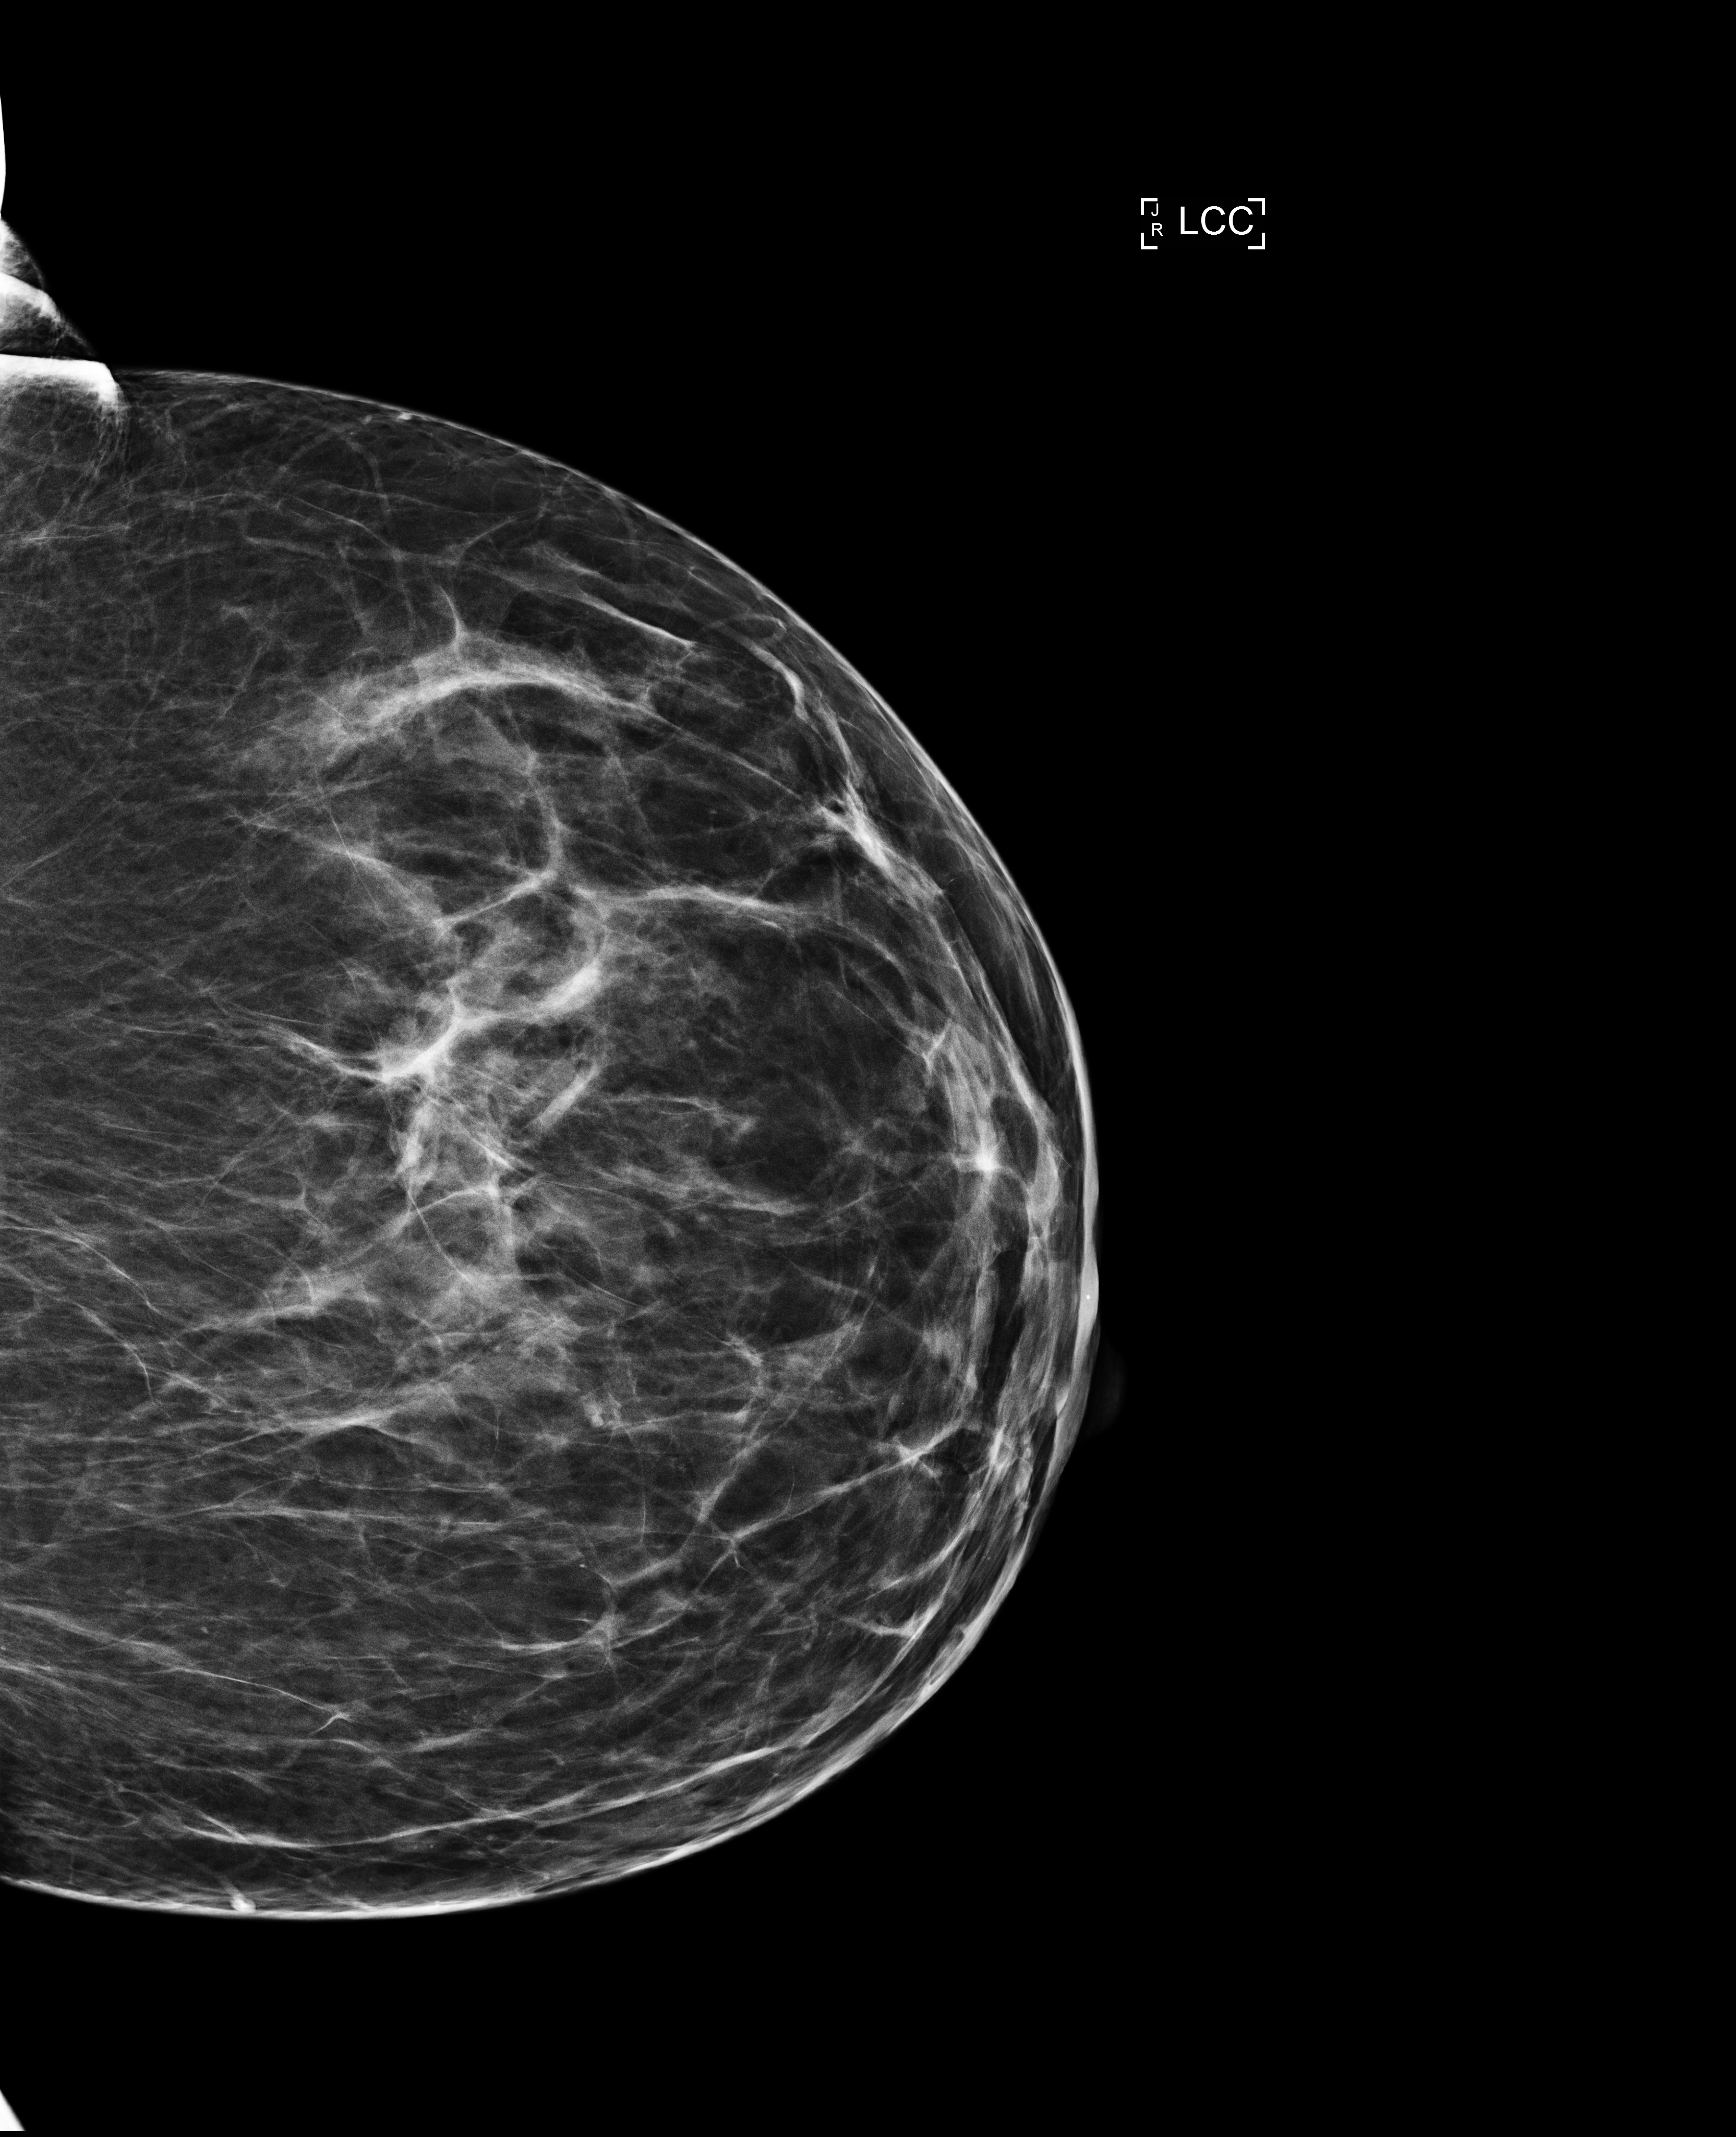
Annual screening mammography examination; compressed breast thickness 63 mm. Female patient, age 50 years.
Image type: full-field digital mammogram. Breast: left. Projection: craniocaudal (CC) view.